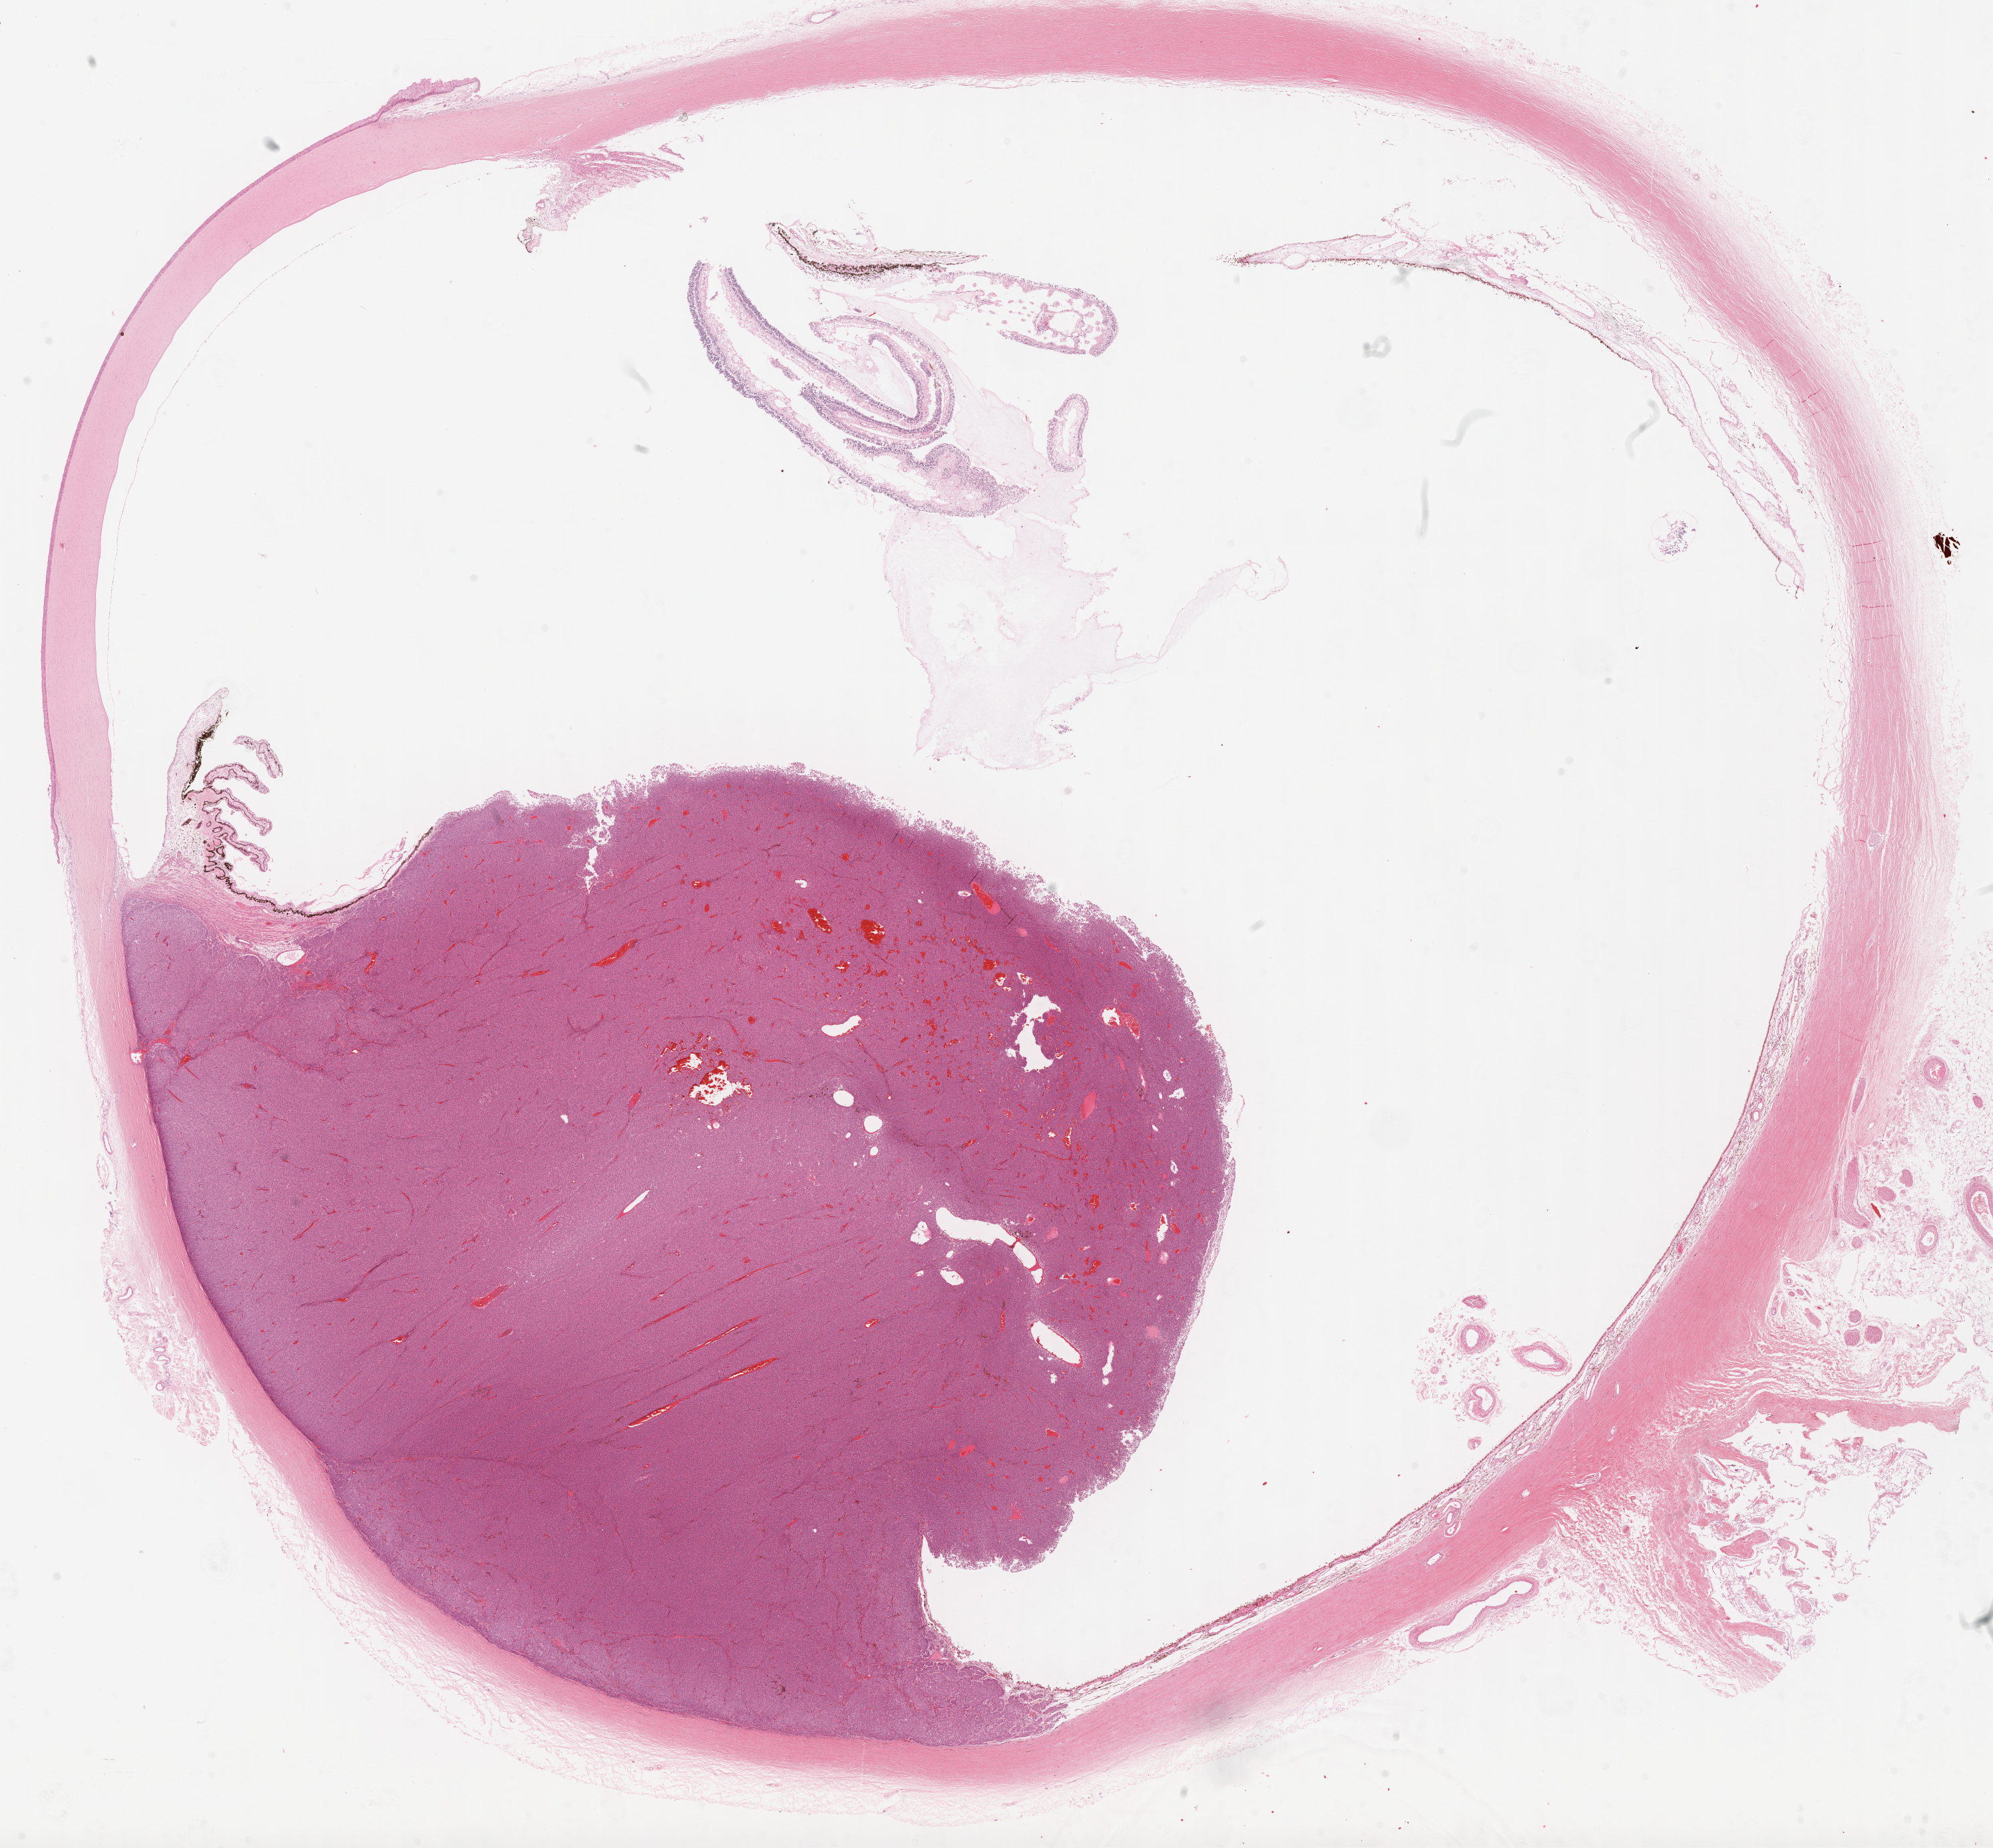
Whole-slide histology image, H&E — a low-resolution overview of the entire scanned area, about 24.1 x 22.4 mm. FFPE section. Uvea, primary tumour sample. Patient: male, age at initial diagnosis 69 years.
* AJCC pathologic stage: IIIB (7th edition)
* pathologic diagnosis: Mixed epithelioid and spindle cell melanoma (overlapping lesion of eye and adnexa)